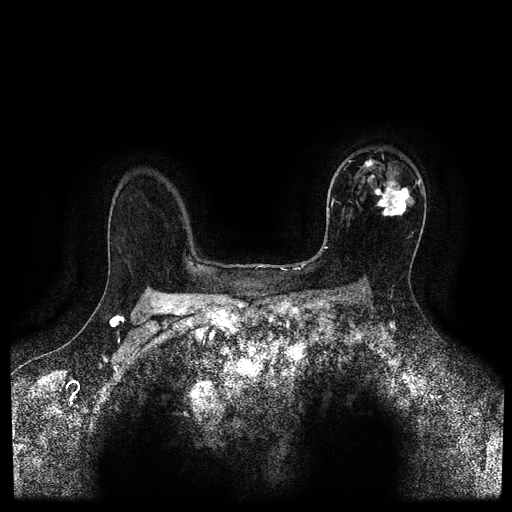
Breast MRI (dynamic contrast-enhanced, multi-phase), one axial slice. Dynamic contrast-enhanced series, time point 2 of 5 at this slice position (early post-contrast). 1.5 T. TE 2.7 ms, TR 5.4 ms. 512 × 512 image matrix, field of view 340 × 340 mm. Female patient, age 50 years.
Outlined on this slice (semi-automatic segmentation, software-assisted and operator-edited):
- breast lesion (labelled 'tumour' in the annotation; benign lesions carry a separate 'benign' label): bounding box [x1, y1, x2, y2] px = [367, 174, 412, 218]
- breast lesion (labelled 'tumour' in the annotation; benign lesions carry a separate 'benign' label): [362, 158, 376, 169]